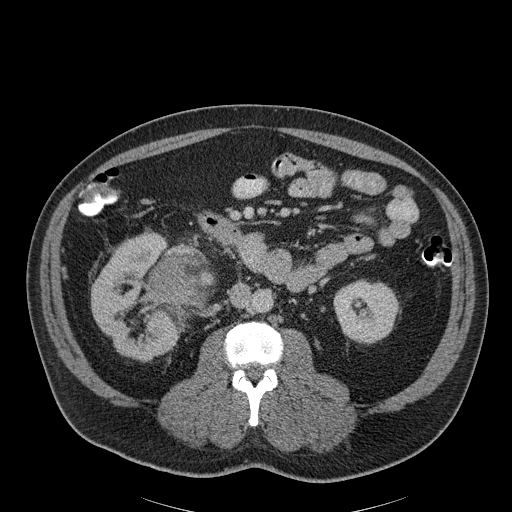
Contrast-enhanced abdominal CT, one axial slice. Position 104 of 186 along the scan axis. Reconstruction kernel B30f. 120 kVp. Soft-tissue window (W 400 / L 40 HU). 3 mm slice thickness. 512 × 512 image matrix, field of view 464 × 464 mm. Male patient, age 56 years. Case-level facts recorded for this patient, not image findings: diagnosis: adrenocortical carcinoma; tumour side: right adrenal; tumour size at pathology: 18 cm; Ki-67 index: 2 %; stage (as recorded): 3.
Structures marked on this image (semi-automatically segmented with operator editing):
- mass: bounding box [x1, y1, x2, y2] px = [153, 259, 209, 307]